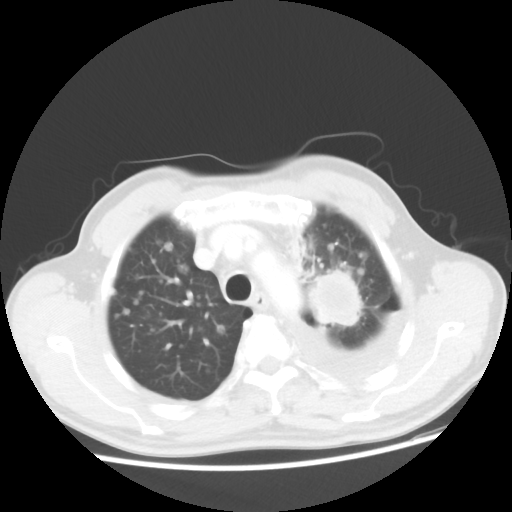
Chest CT, one axial slice. Slice 38 of 48 in the series (ordered by position). Reconstruction kernel STANDARD. 100 kVp. Lung window (W 1500 / L -600 HU). 5 mm slice thickness. 512 × 512 image matrix, field of view 362 × 362 mm. Patient: male, 55 years. From the clinical record (not read from this slice): clinical TNM (as recorded): T2 N3 M1a; histopathological grade: G3.
Outlined on this slice (bounding box drawn by a radiologist):
- lung tumour (recorded histology: squamous cell carcinoma): box from (x=307, y=265) to (x=363, y=339) px